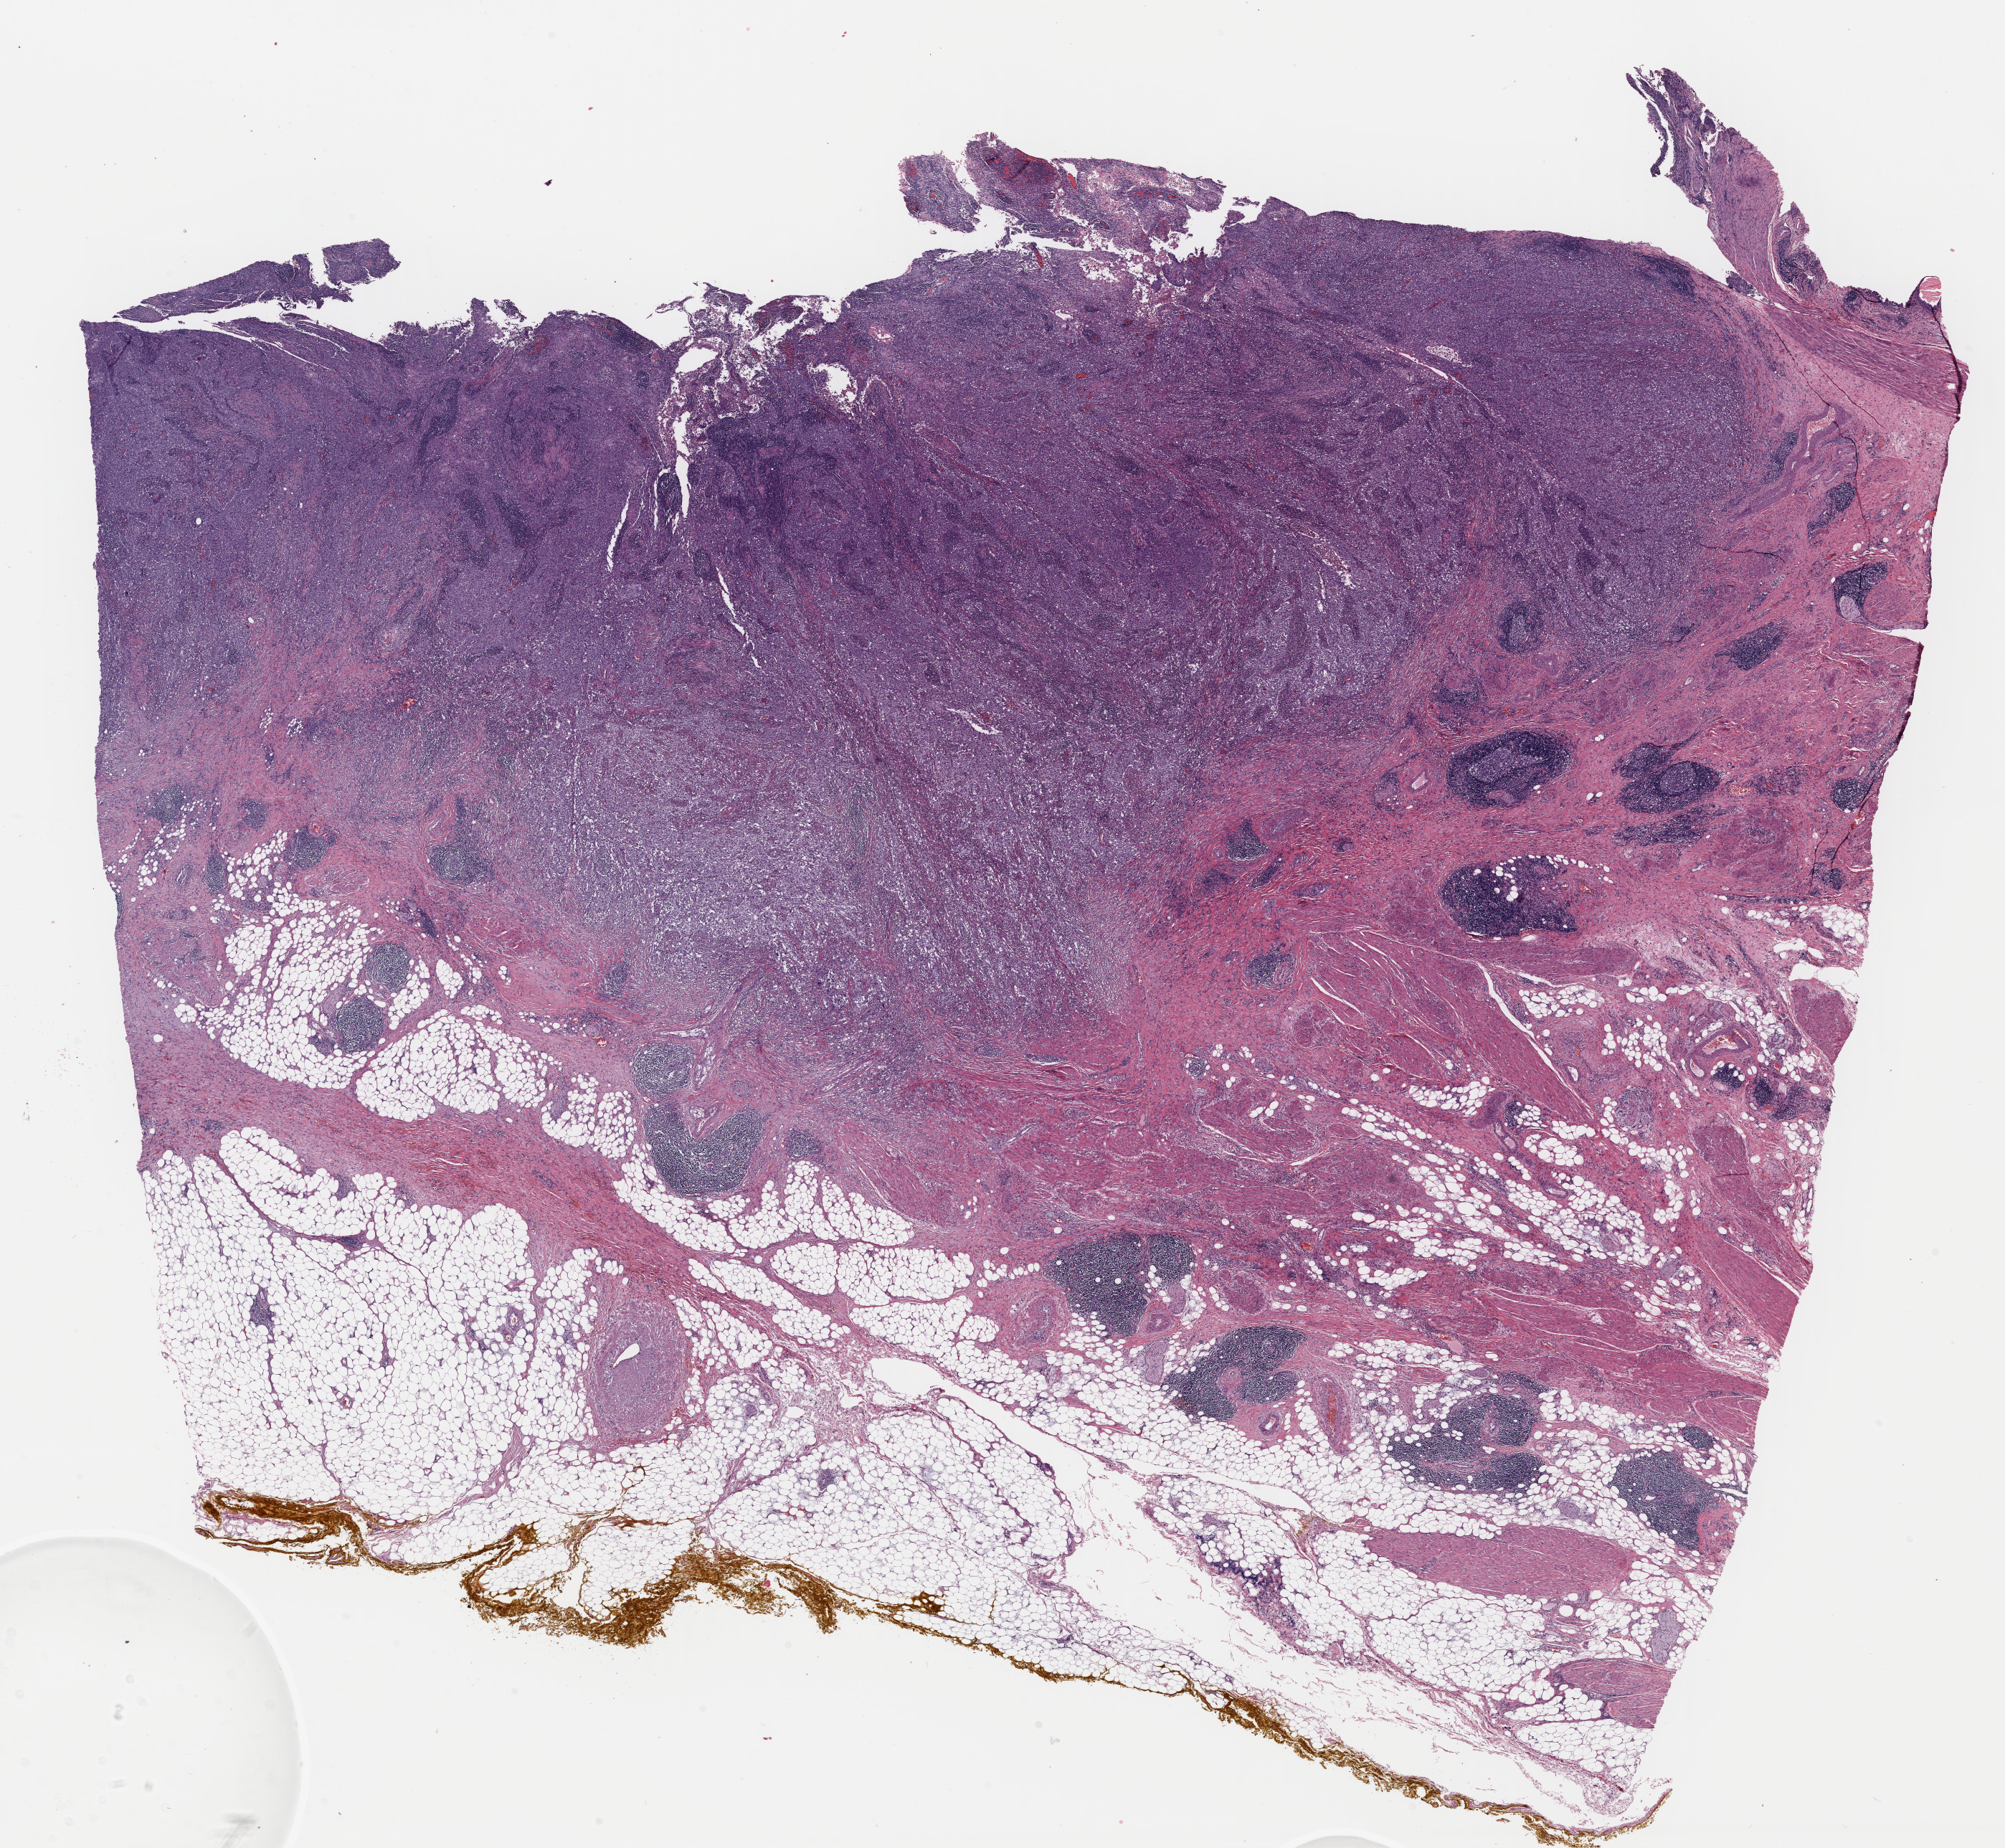
Whole-slide histology image, H&E-stained — whole scanned area (about 22.0 x 20.3 mm, slide scanned at 40x) shown as a low-resolution overview. Formalin-fixed paraffin-embedded (FFPE) diagnostic section. Bladder, primary tumour sample. Male, age 74 years at initial diagnosis. Histologic grade: high grade.
* AJCC pathologic stage: III (7th edition)
* diagnosis: Papillary transitional cell carcinoma